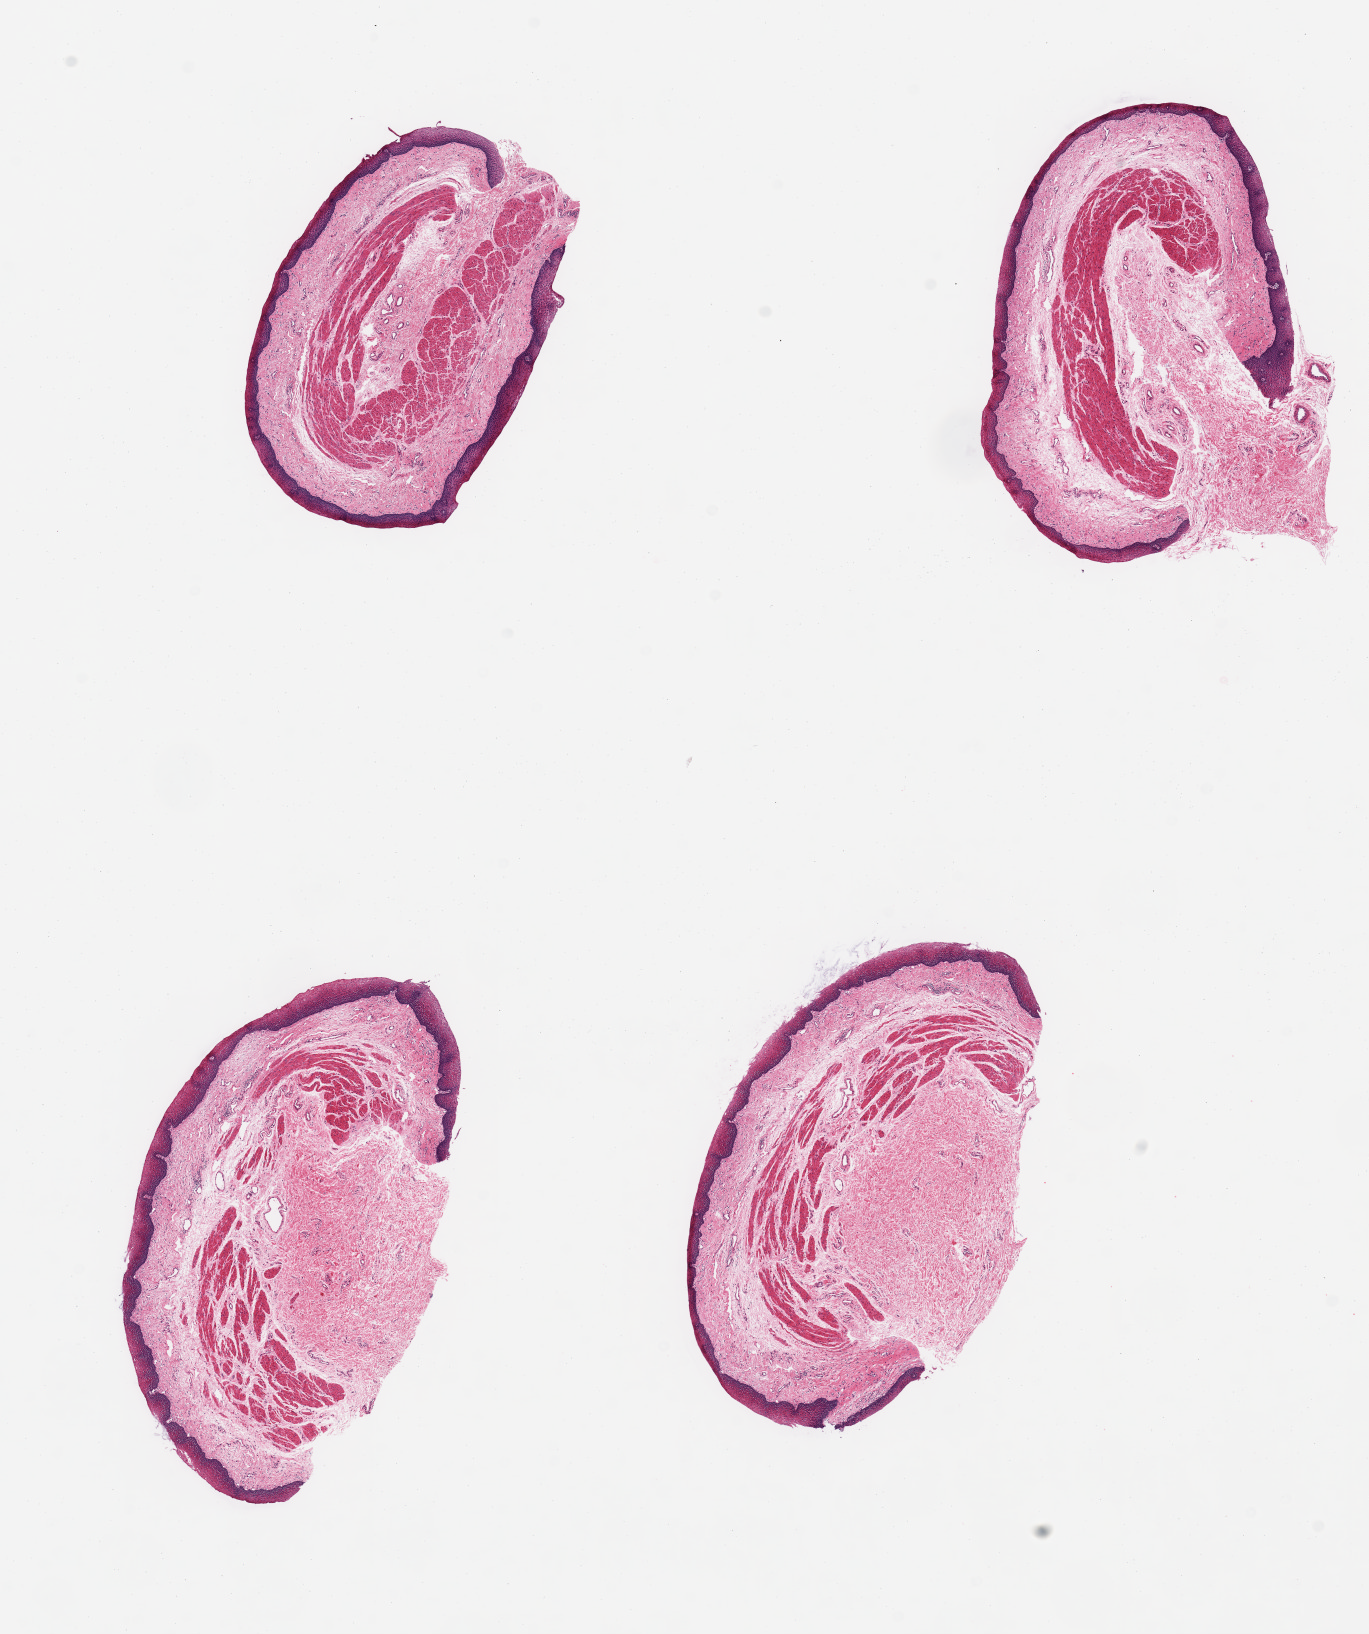
Haematoxylin and eosin whole-slide image, whole scanned area (about 10.8 x 12.9 mm) shown as a low-resolution overview. PAXgene-fixed paraffin-embedded (PFPE) section. Sampled site (target tissue): esophageal mucous membrane. Donor tissue sample. Donor sex: female.
Review note (as recorded): 4 pieces; slight sloughing of surface on 2 pieces; slightly edematous stroma; abundant submucosal fibrous stroma, without glands.